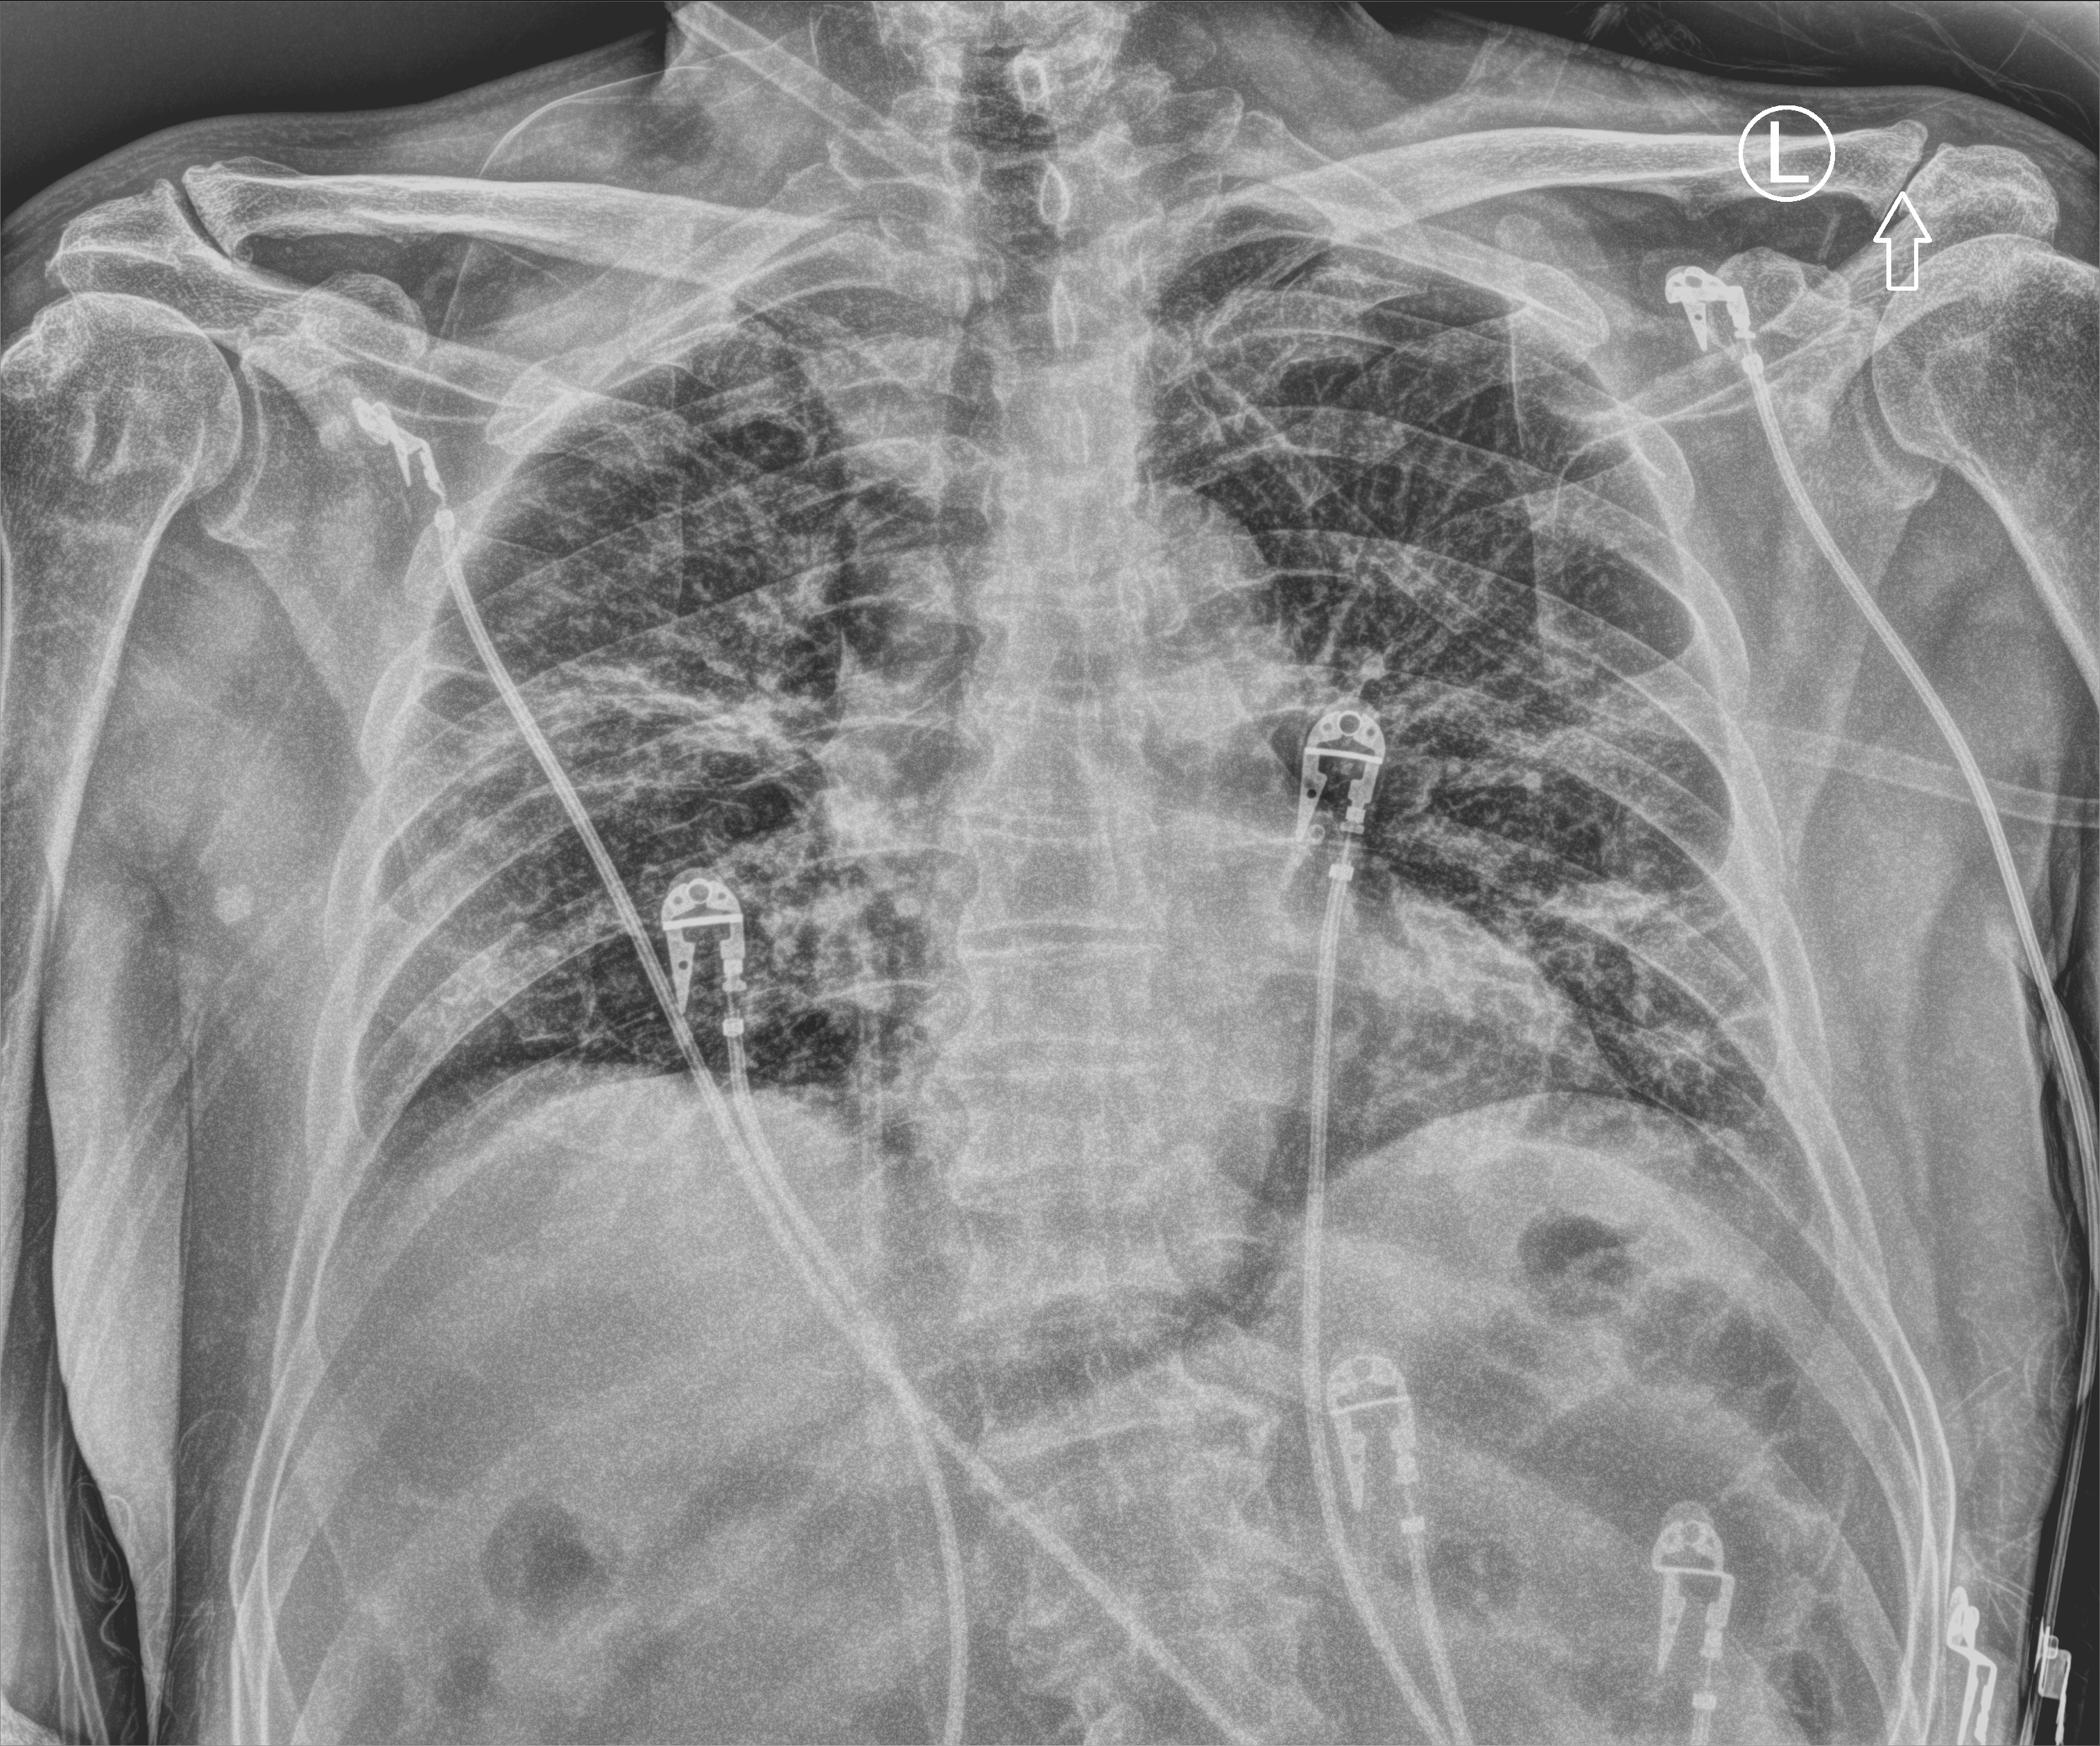
Chest X-ray (portable); anteroposterior (AP) projection. Male patient hospitalised with COVID-19, age 60–74 years.
Admission-level facts for this patient (not findings on this image; timing relative to this image not recorded): hypertension (admission record): yes; admitted to intensive care during this hospital stay: no.